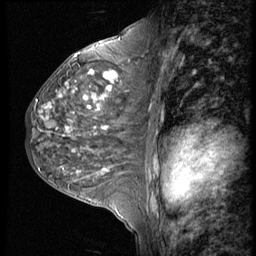
Breast MRI (dynamic contrast-enhanced), one sagittal slice; slice 28 of 56 in the series (ordered by position); 4 images stored at this slice position (order not interpretable as contrast timing); 1.5 T; TE 4.2 ms, TR 9 ms; 2.5 mm slice thickness; 256 × 256 image matrix. Female patient, age 50 years. From the clinical record (not read from this slice): setting: breast cancer imaged before/during neoadjuvant chemotherapy; receptor status: triple-negative.
Annotated regions visible in this slice (semi-automatic segmentation, software-assisted and operator-edited):
- analysis volume of interest (the breast-tissue region the enhancement analysis was run in; not a lesion): bounding box (x1, y1, x2, y2) in pixels: (25, 46, 148, 188)
- tumour enhancement mask (voxels above the 140 % enhancement threshold inside the analysis volume of interest): (36, 56, 120, 131)